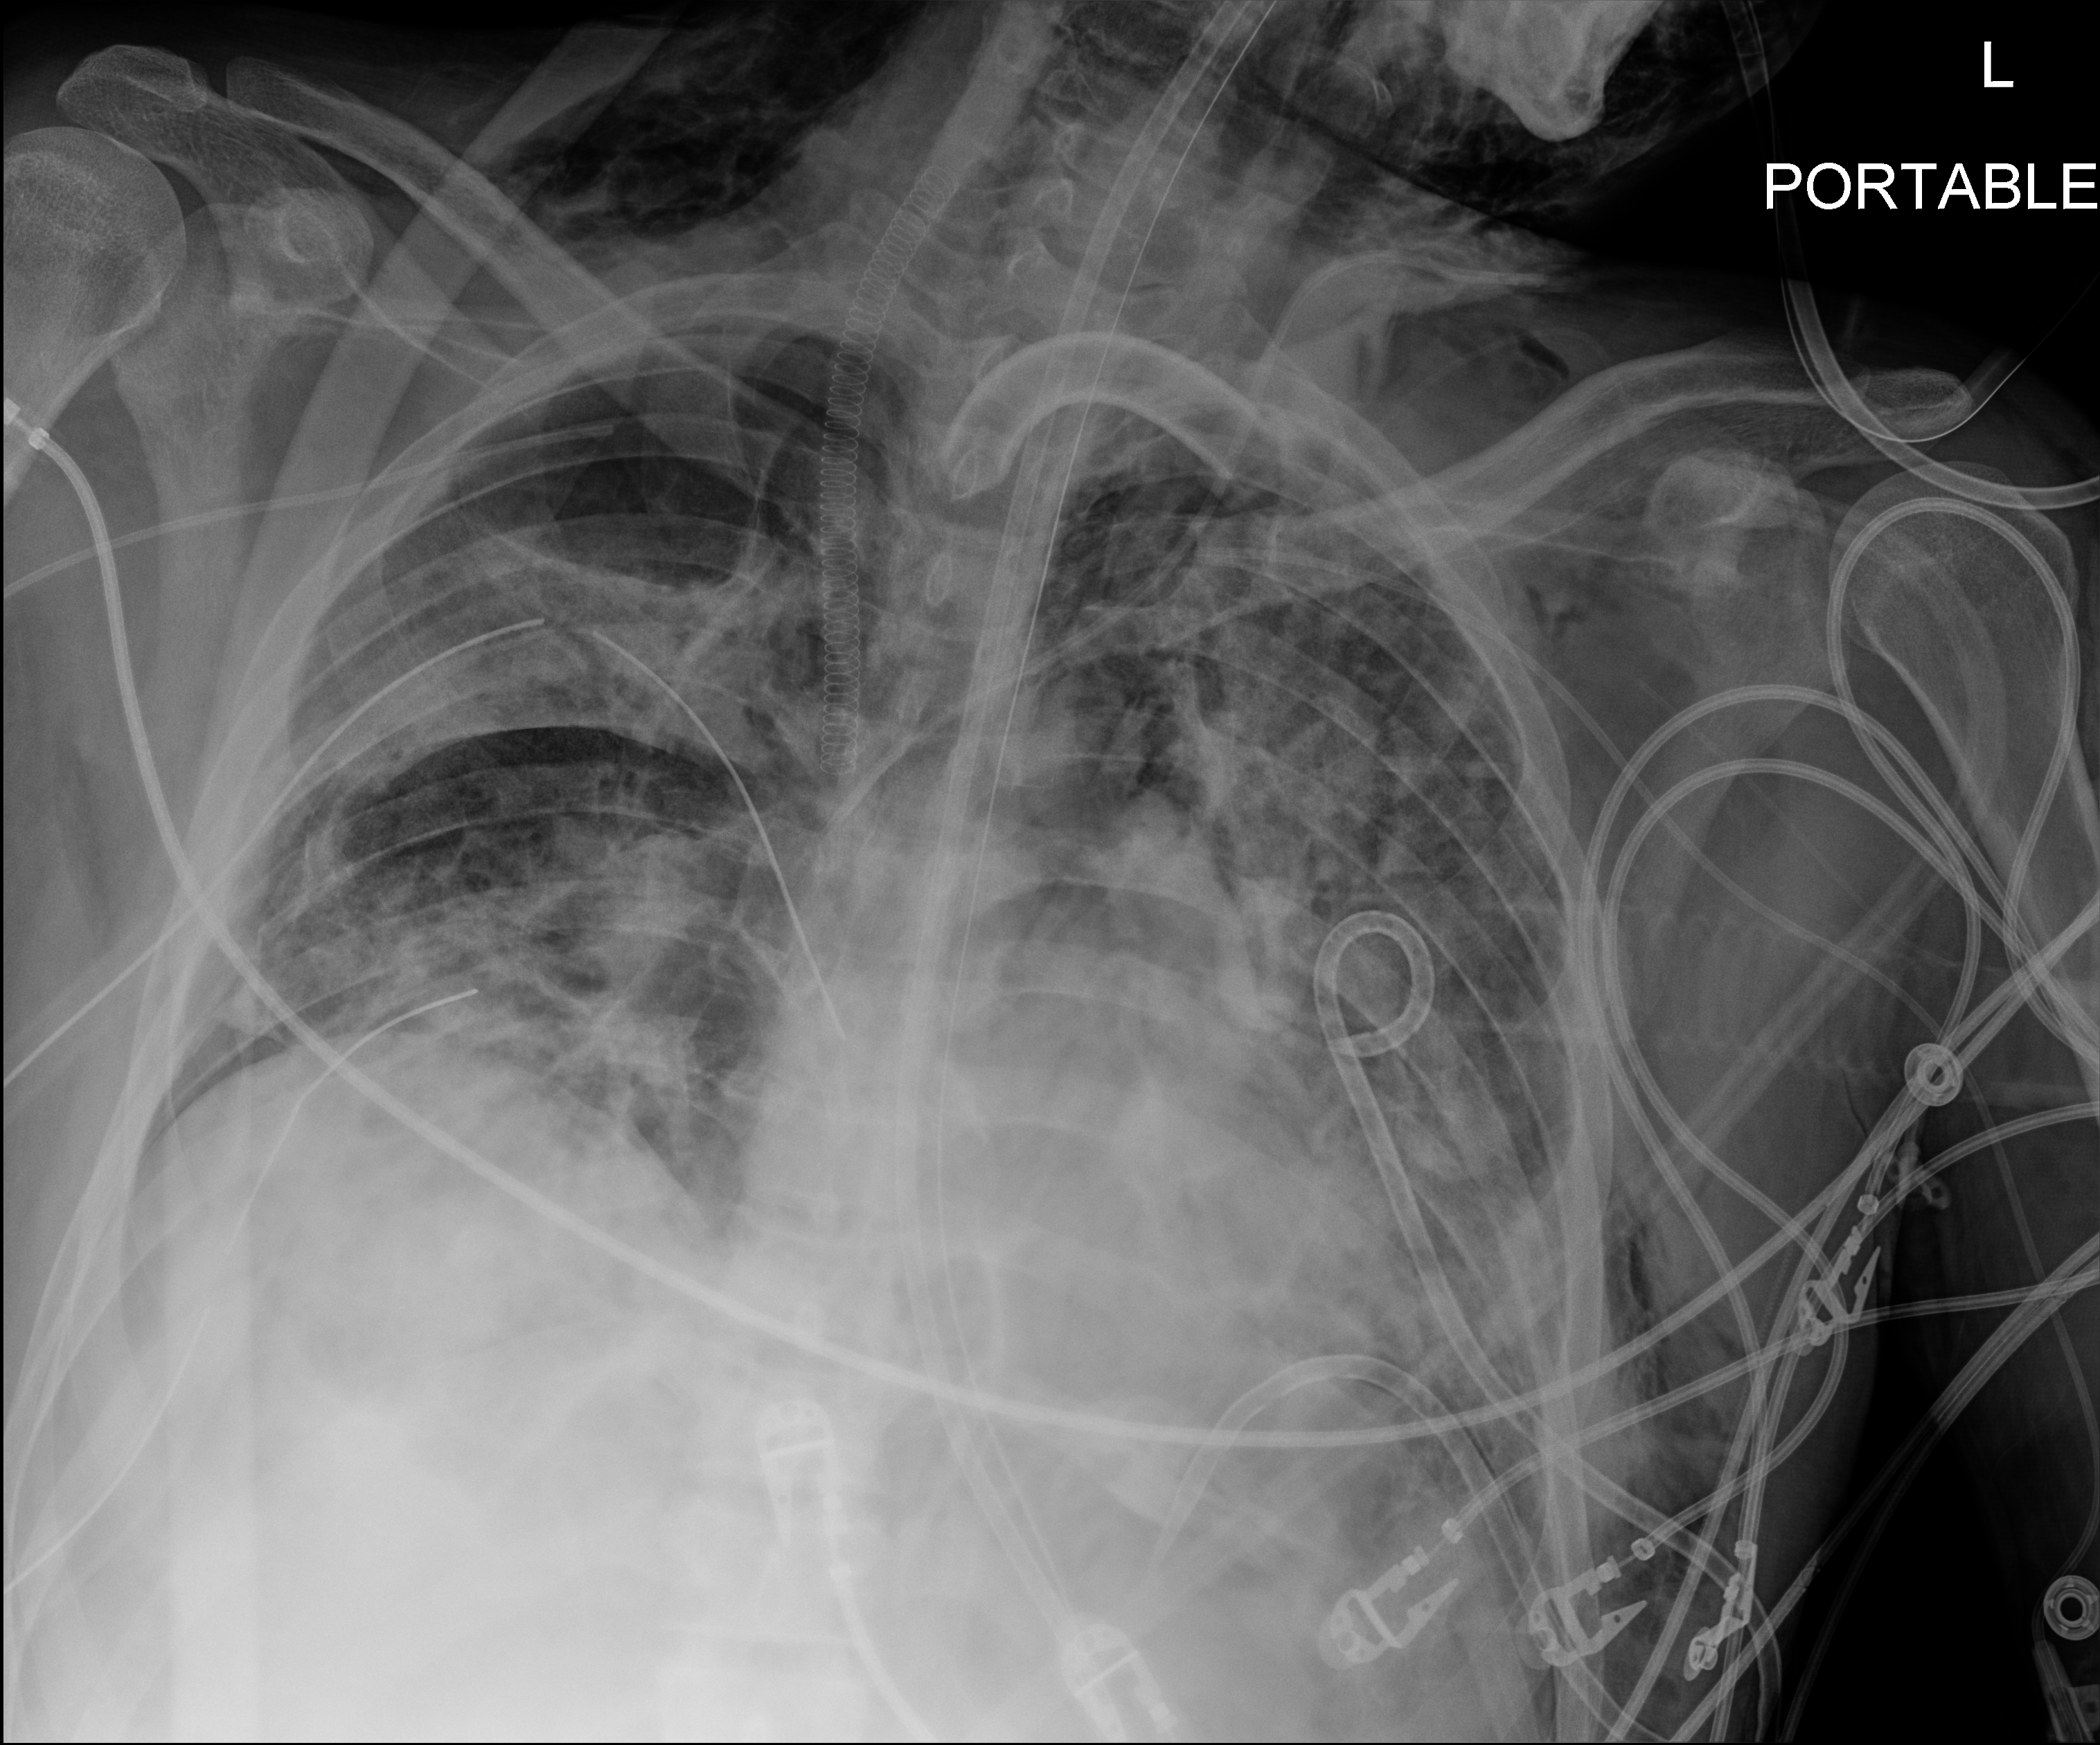
Chest X-ray (portable); anteroposterior (AP) projection. Adult patient hospitalised with COVID-19, age 18–59 years.
Admission-level facts for this patient (not findings on this image; timing relative to this image not recorded): admitted to intensive care during this hospital stay: yes; mechanically ventilated during this hospital stay: yes; length of hospital stay: 60 days.